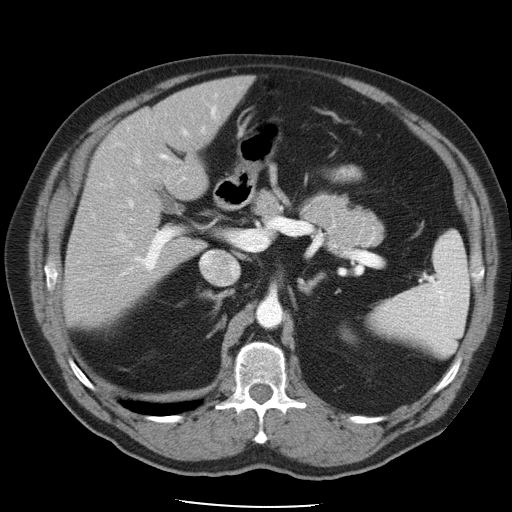
Contrast-enhanced abdominal CT, one axial slice. Slice 29 of 49 in the series (ordered by position). 120 kVp. Soft-tissue window (W 400 / L 40 HU). 5 mm slice thickness. 512 × 512 image matrix, field of view 395 × 395 mm. Male patient, age 68 years. Case-level facts recorded for this patient, not image findings: diagnosis: colorectal cancer liver metastases, imaged before liver resection; multiple liver metastases: yes.
Structures marked on this image (outlined manually by an expert reader):
- hepatic veins: box from (x=111, y=154) to (x=238, y=284) px
- liver: (x=66, y=77)–(x=249, y=325)
- planned liver remnant (the part of the liver to remain after resection): (x=67, y=77)–(x=250, y=326)
- portal vein (with intrahepatic branches): (x=93, y=95)–(x=217, y=276)